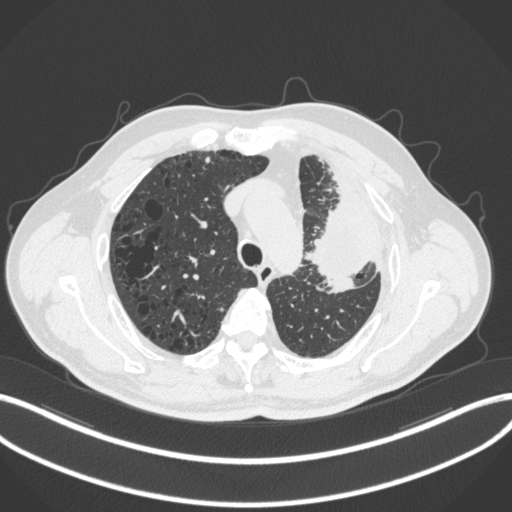
Chest CT, one axial slice; position 229 of 286 along the scan axis; reconstruction kernel B31f; lung window (W 1500 / L -600 HU); 1 mm slice thickness; 512 × 512 image matrix, field of view 400 × 400 mm. Patient: male, 68 years. From the clinical record (not read from this slice): clinical TNM (as recorded): T3 N3 M1.
Outlined on this slice (bounding box drawn by a radiologist):
- lung tumour (recorded histology: adenocarcinoma): bounding box [x1, y1, x2, y2] px = [301, 192, 372, 293]